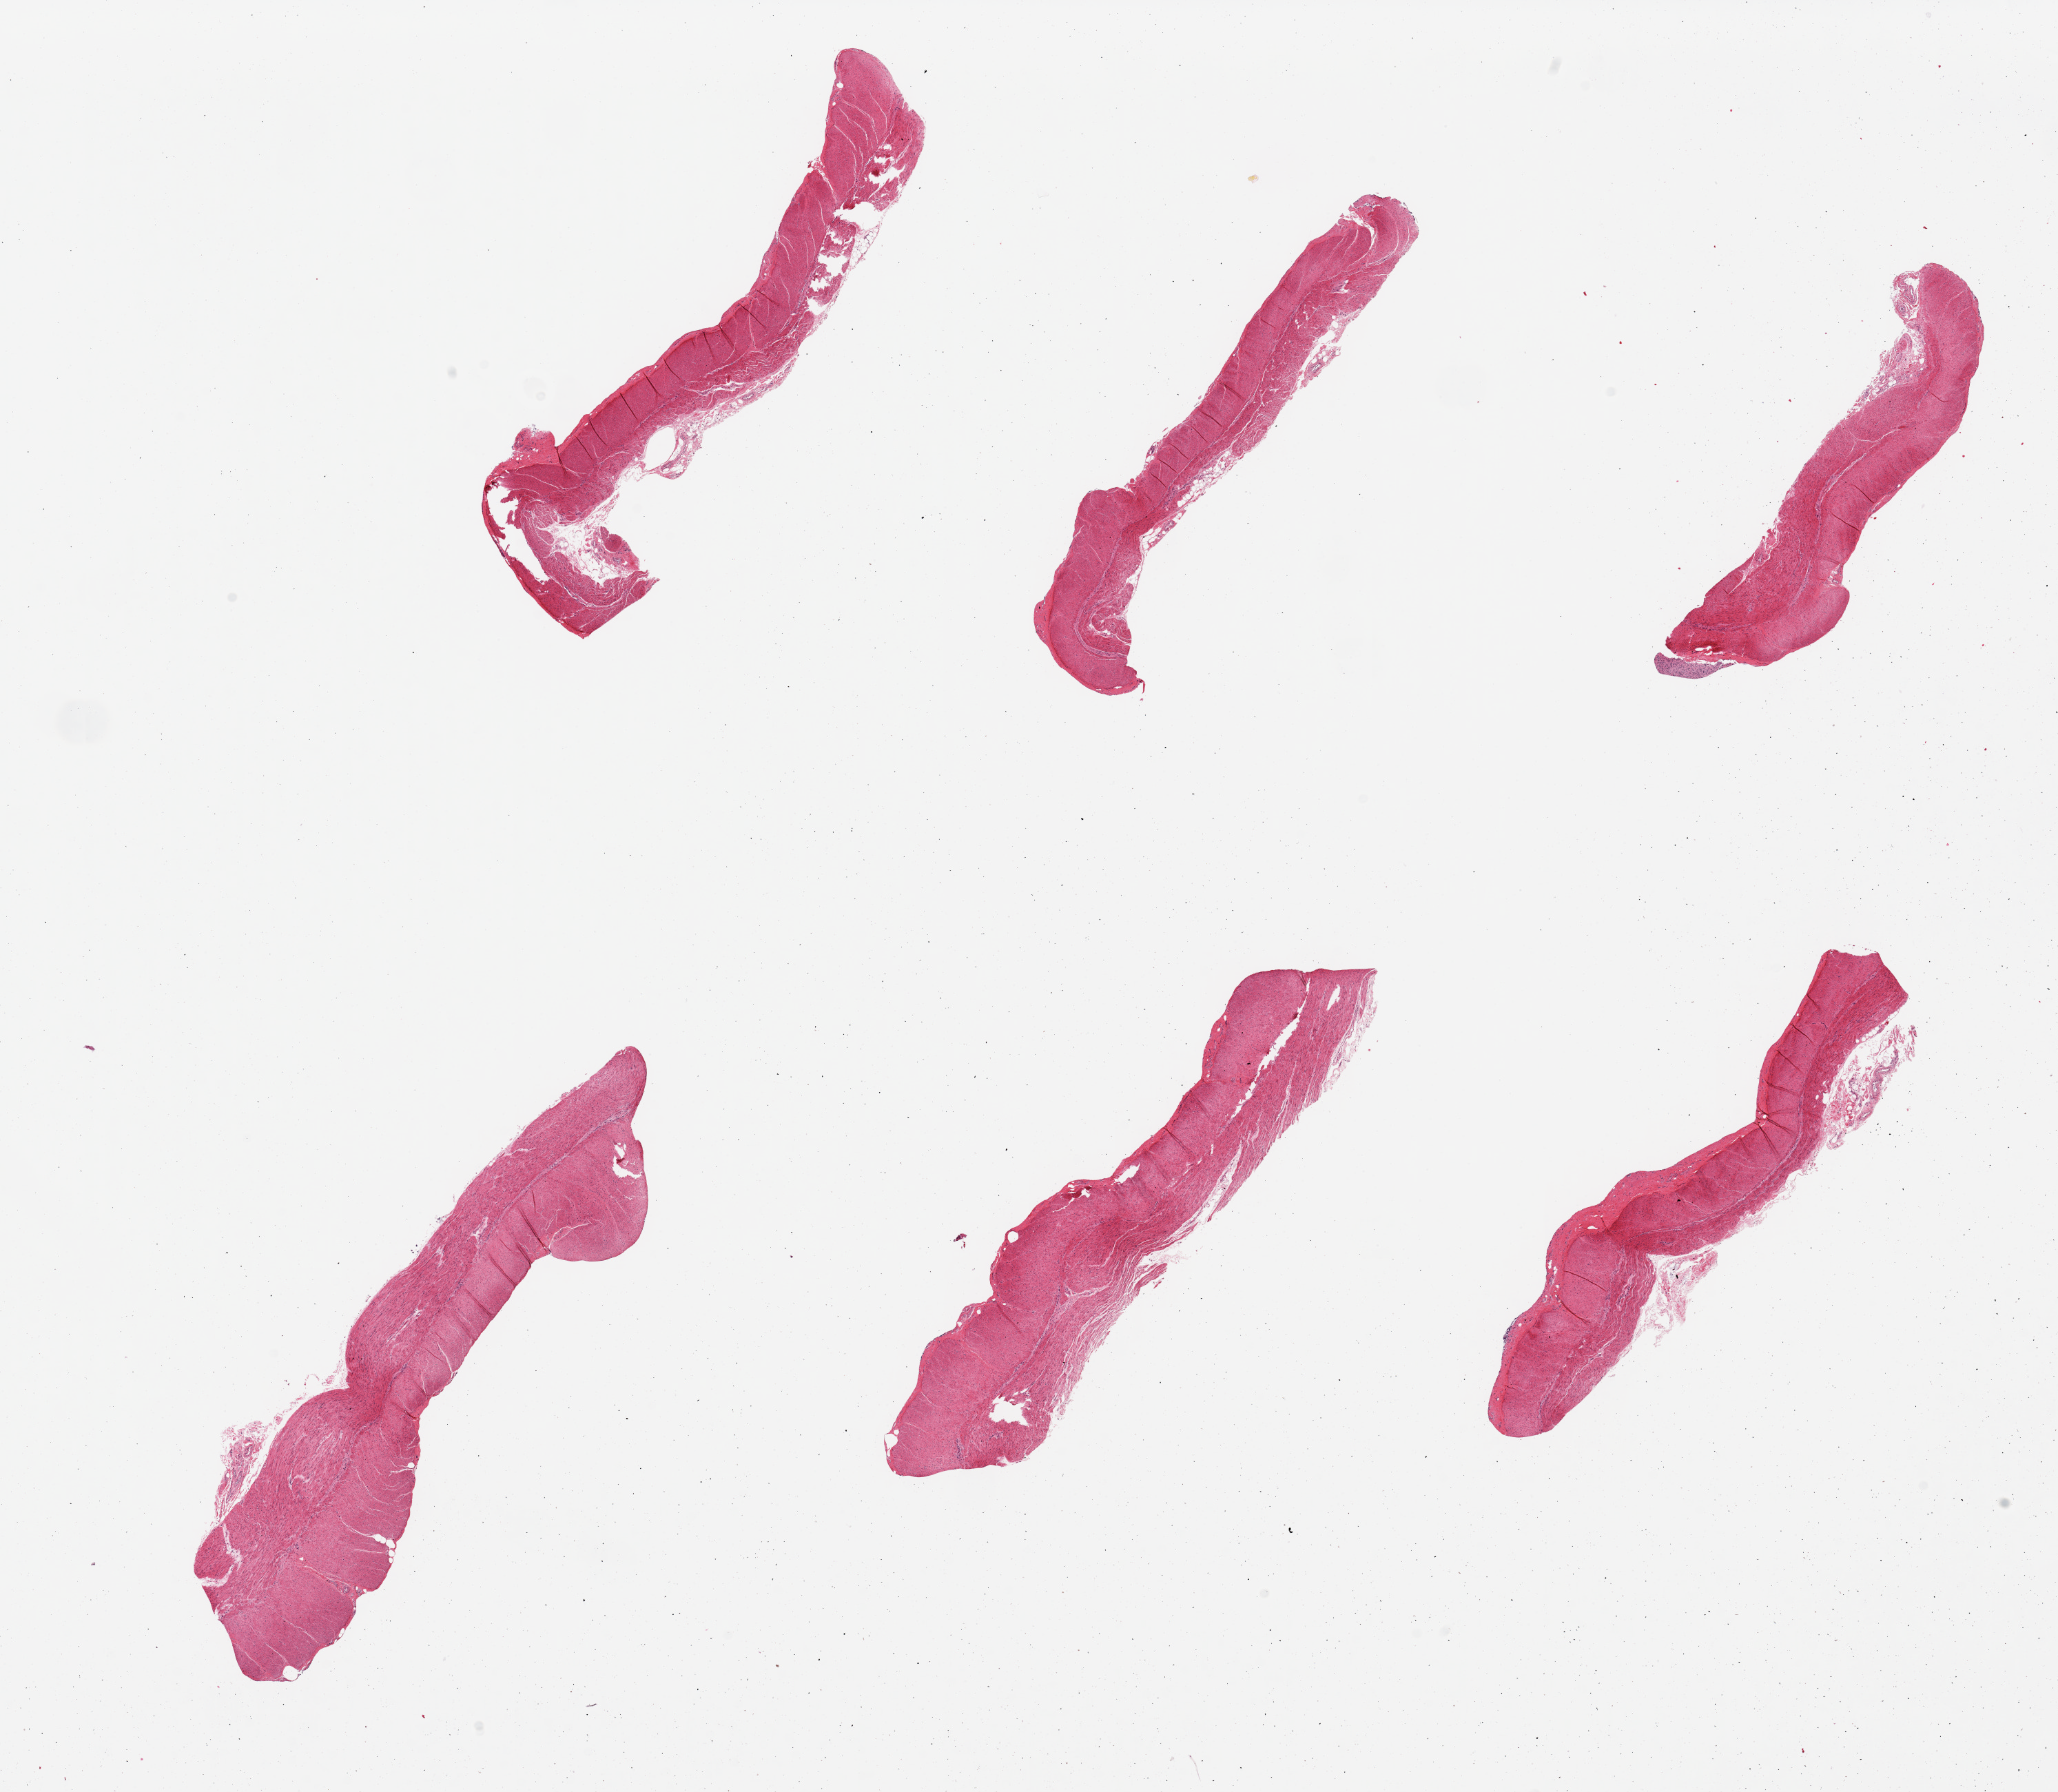
Hematoxylin and eosin (H&E) whole-slide image, brightfield, shown as a low-resolution overview of the whole scanned area (about 23.6 x 20.6 mm); PAXgene-fixed, paraffin-embedded tissue; target tissue: sigmoid colon; tissue donor sample. Female donor.
Reviewer comment on this tissue sample: 6 pieces; well dissected muscularis.